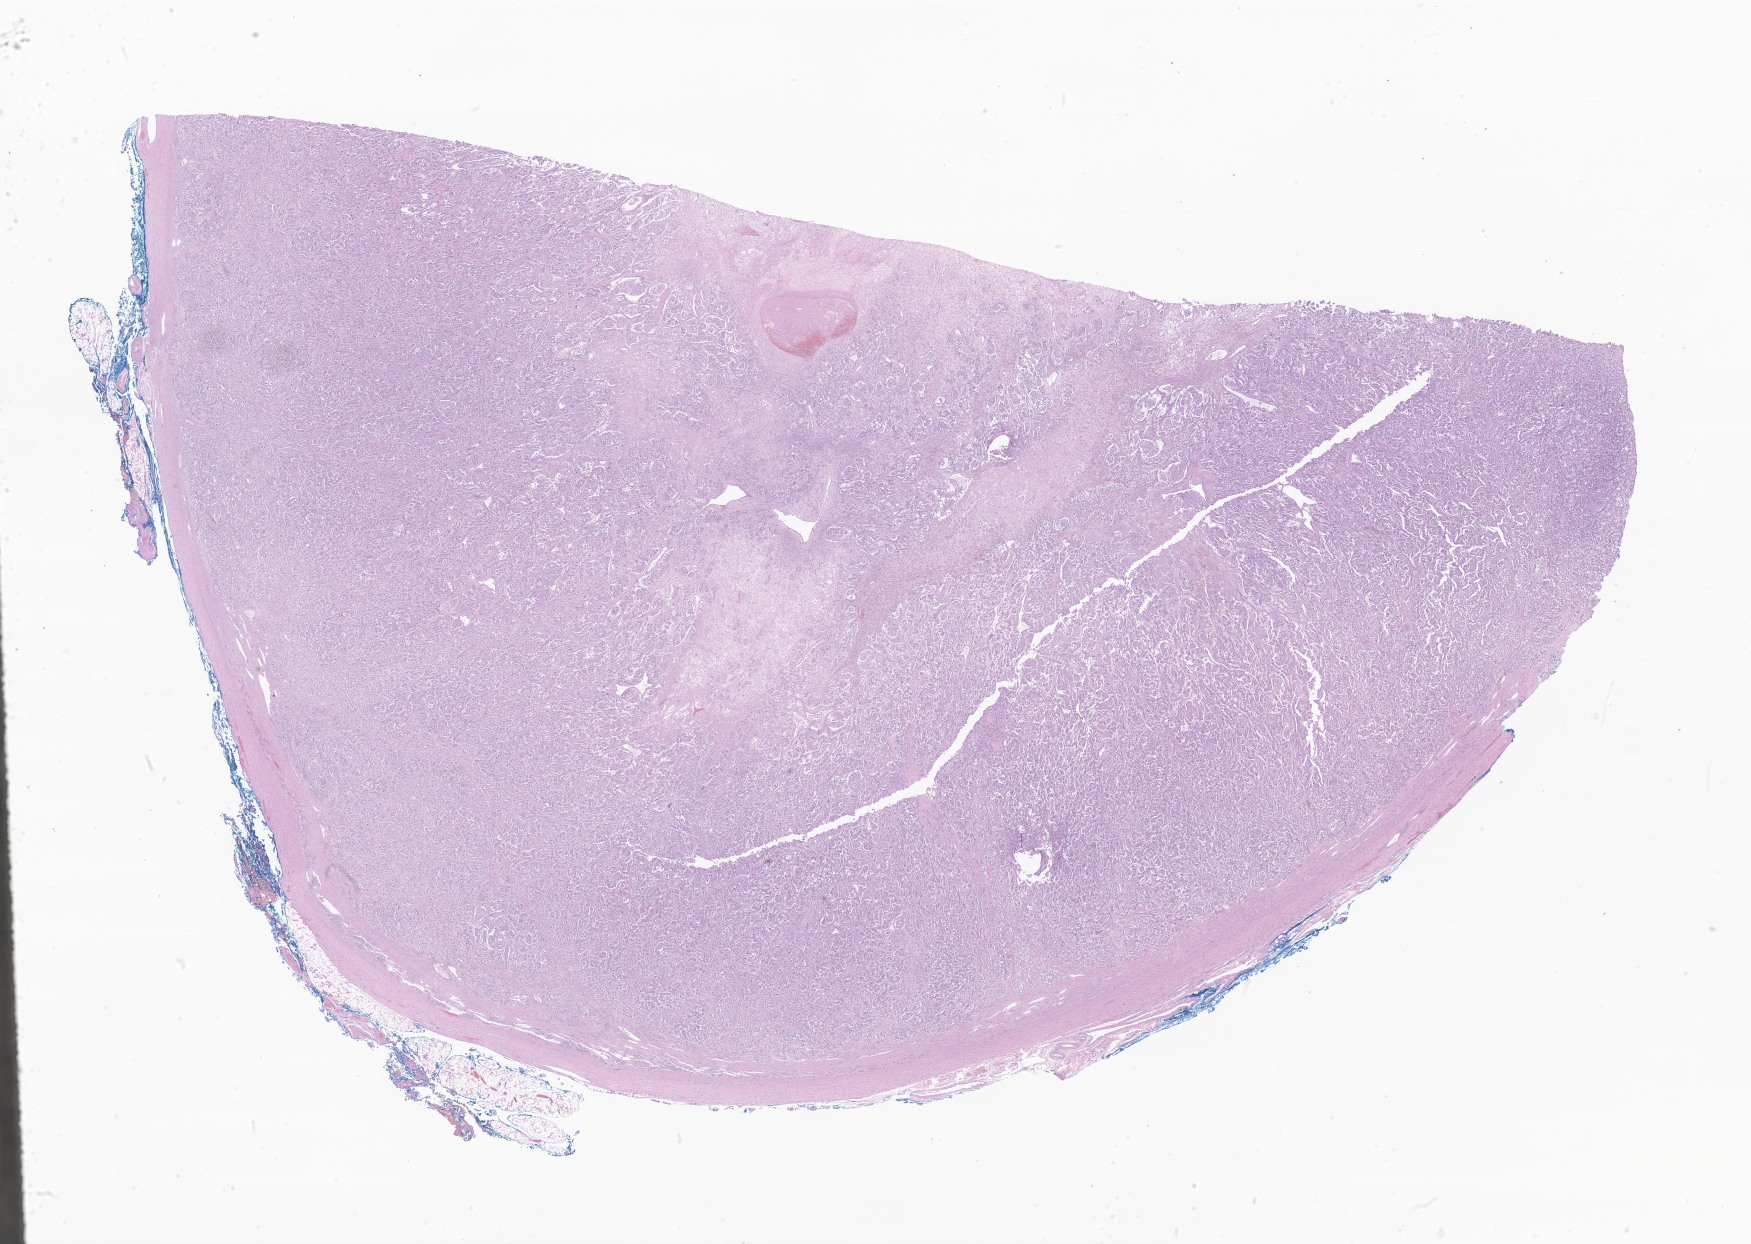
Whole-slide image, haematoxylin and eosin stain of tumor tissue from the adrenal gland, shown as a low-resolution overview of the whole scanned area (about 29.5 x 21.0 mm). Patient male; age 197 months (16 years 5 months).
Specimen: formalin-fixed, paraffin-embedded (FFPE) tissue.